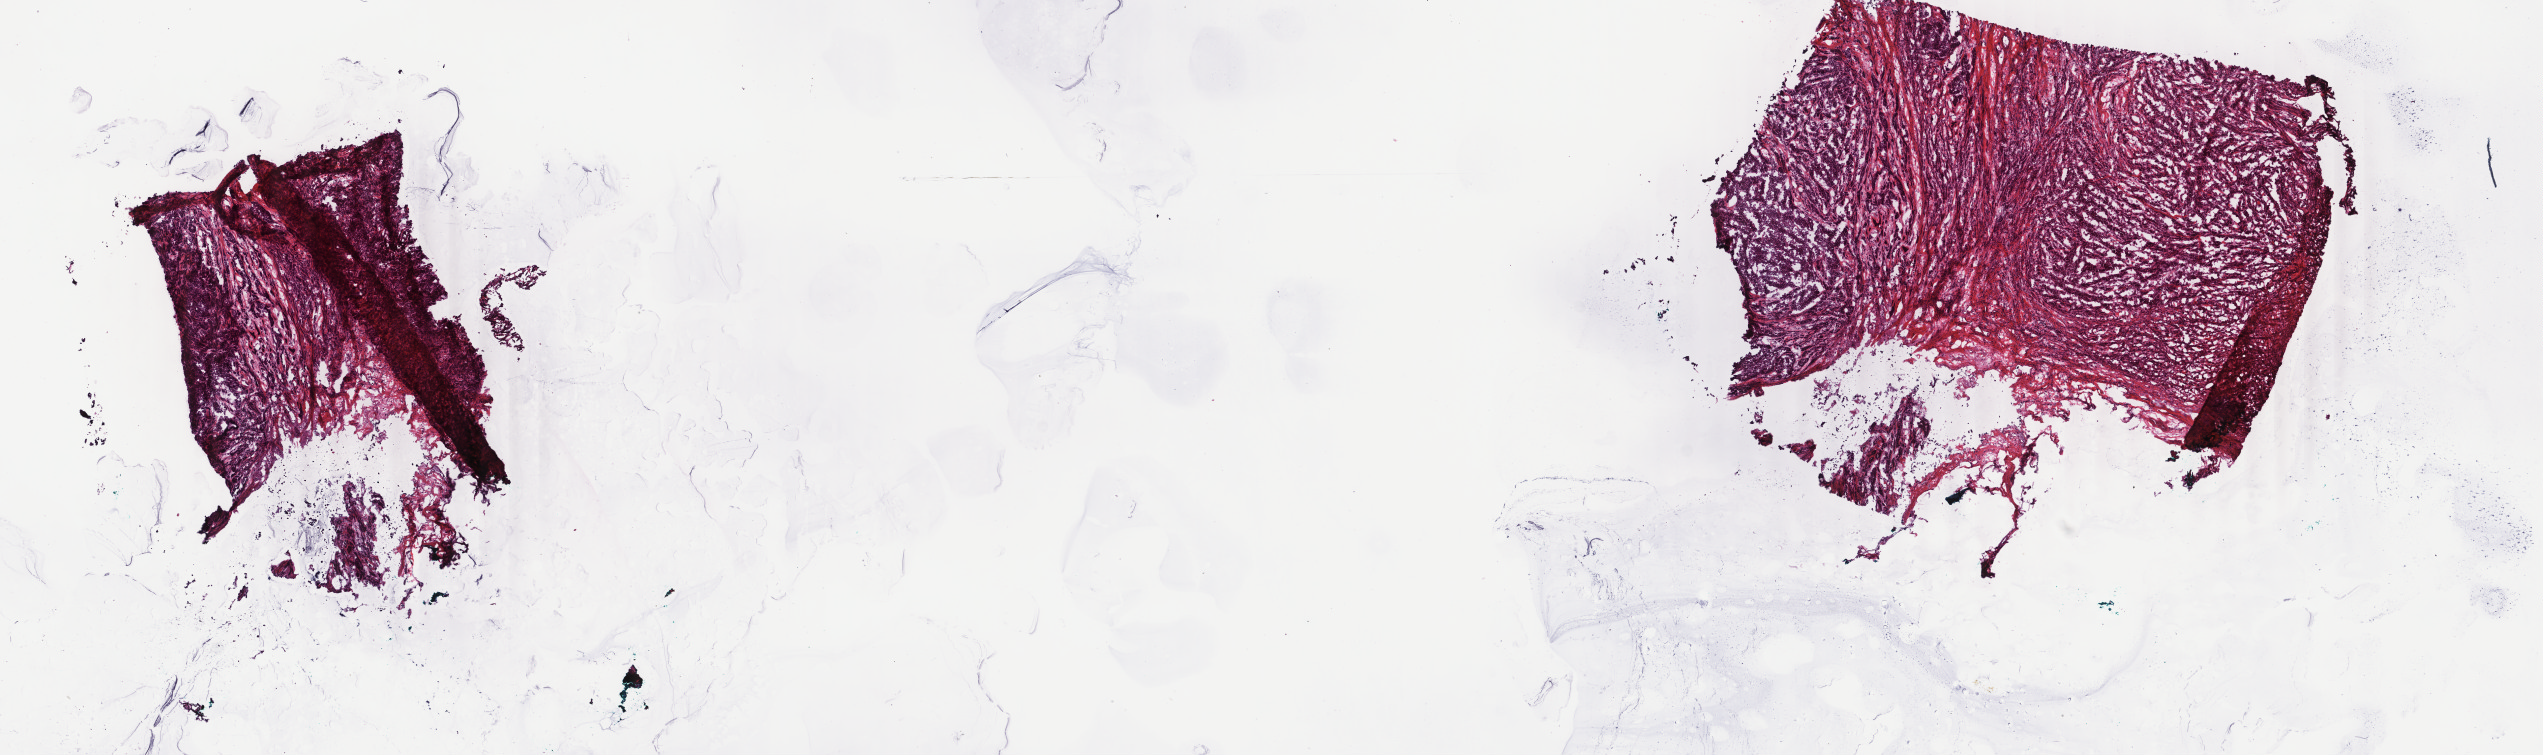
Whole-slide histology image, H&E, shown as a low-resolution overview of the whole scanned area (about 20.2 x 6.0 mm, slide scanned at 40x). Frozen section from the top of the tissue portion. Primary tumour sample from the breast. Patient: female, age at initial diagnosis 61 years. Pathologist review of this section (percent, as recorded): tumour cells 100%, tumour nuclei 90%, normal cells 0%, stromal cells 0%, necrosis 0%. Inflammatory infiltration, as recorded: lymphocyte infiltration 0%, monocyte infiltration 0%, neutrophil infiltration 0%.
AJCC pathologic stage: IIIA (6th edition). Diagnosis: Infiltrating duct carcinoma, NOS. Lymph nodes positive (case pathology): 6 of 24 examined.